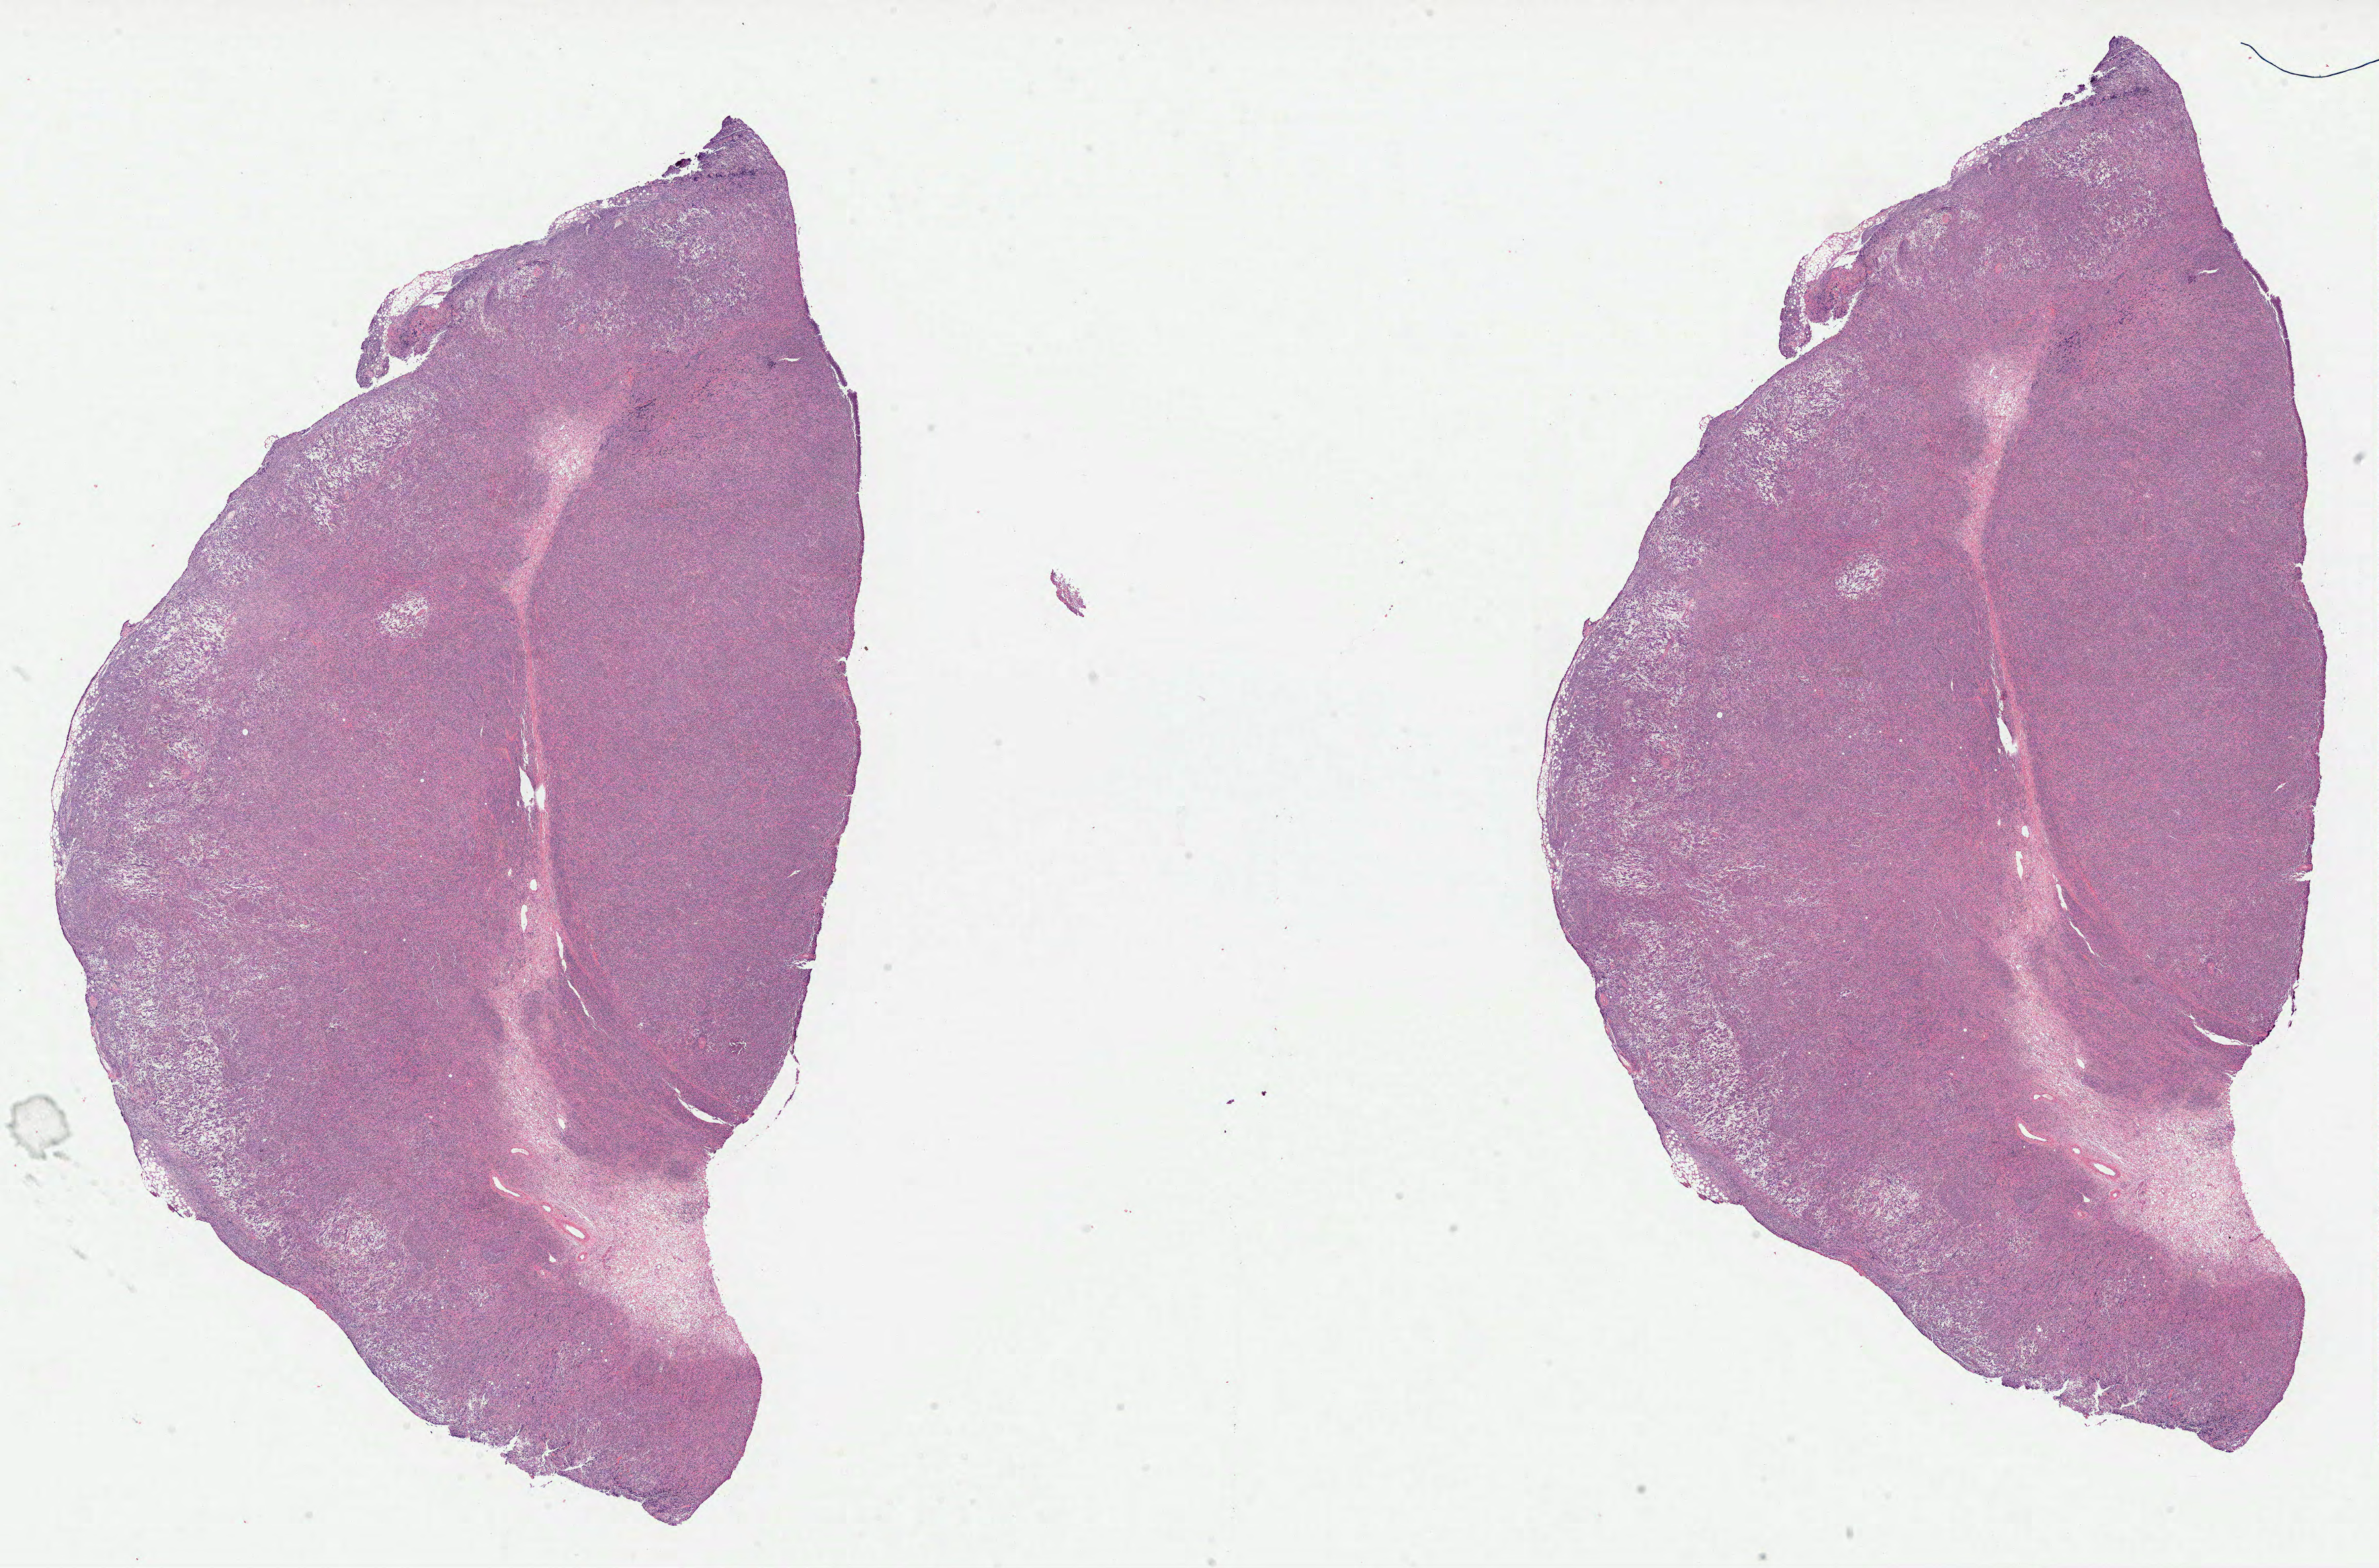
Whole-slide histology image, H&E — shown as a low-resolution overview of the whole scanned area (about 29.0 x 19.1 mm). Formalin-fixed paraffin-embedded (FFPE) diagnostic section. Sample: primary tumour, lymphoid tissue. Male, age 67 years at initial diagnosis.
Pathologic diagnosis: Diffuse large B-cell lymphoma, NOS (lymph nodes of head, face and neck).